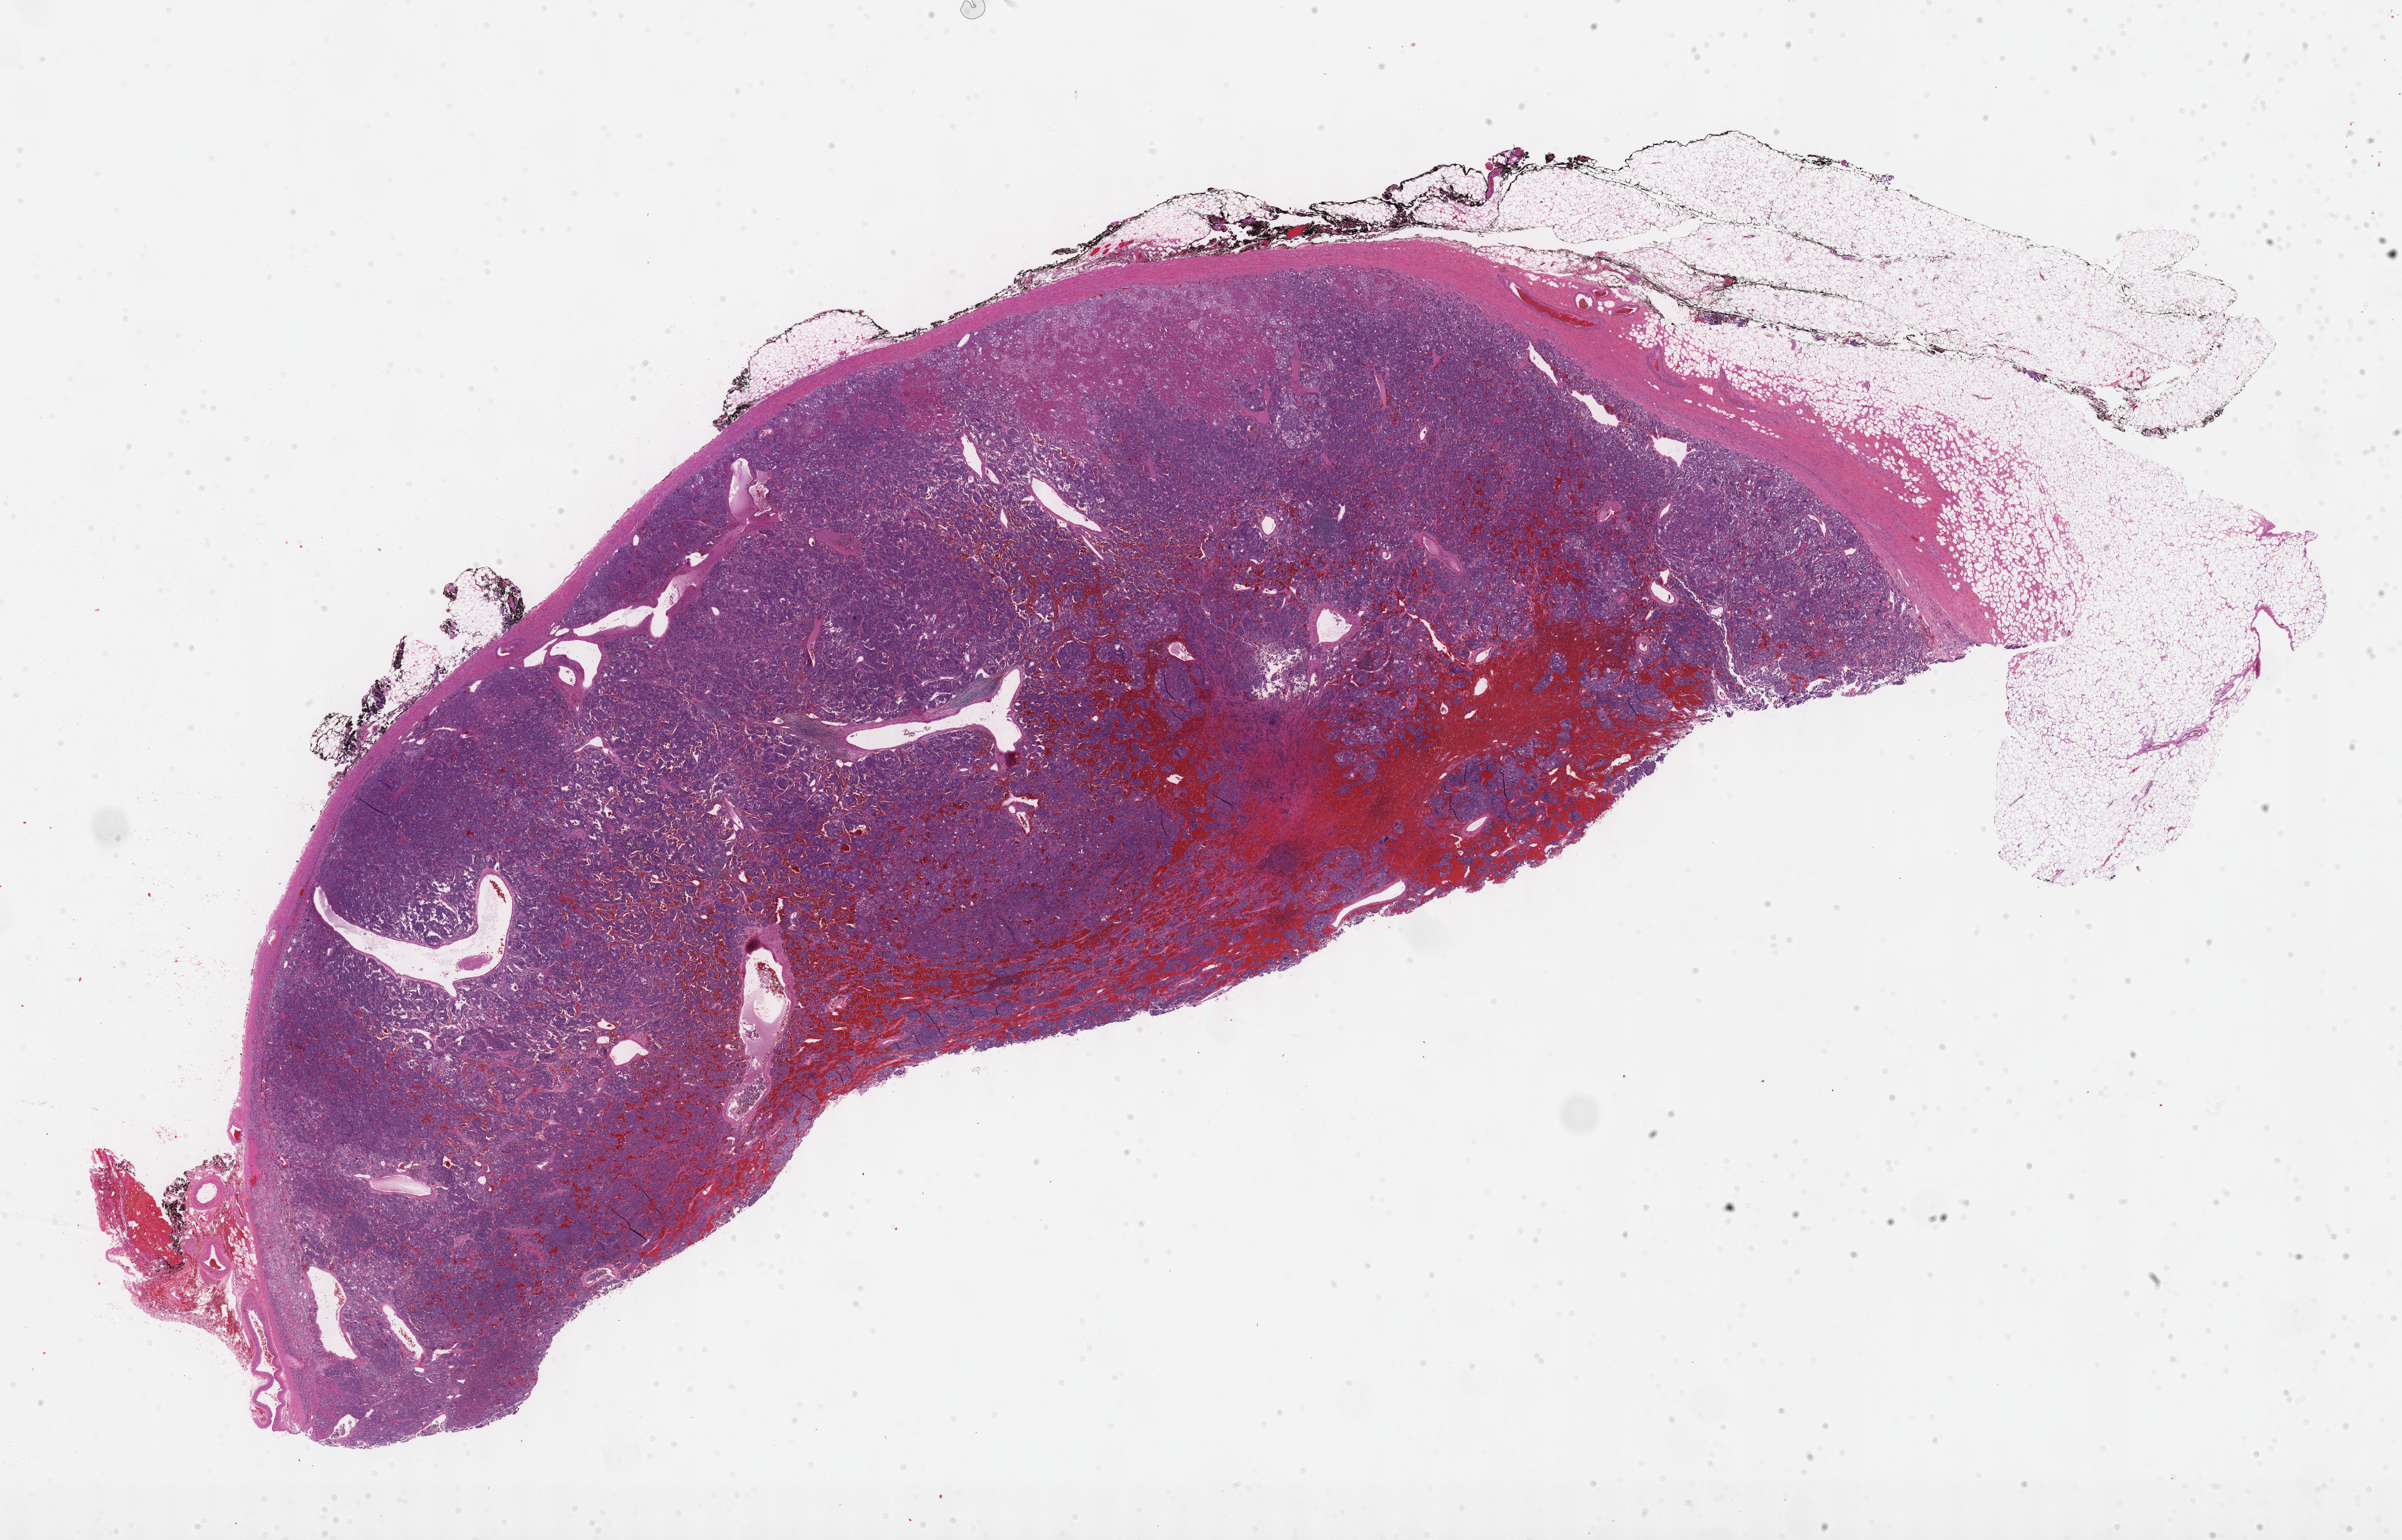
Whole-slide histology image, H&E-stained, low-resolution overview of the scanned area, about 31.2 x 20.0 mm (acquisition: 40x scan). FFPE section. Sample: primary tumour, adrenal gland. Patient: male, age at initial diagnosis 55 years.
Pathologic diagnosis: Pheochromocytoma, NOS.